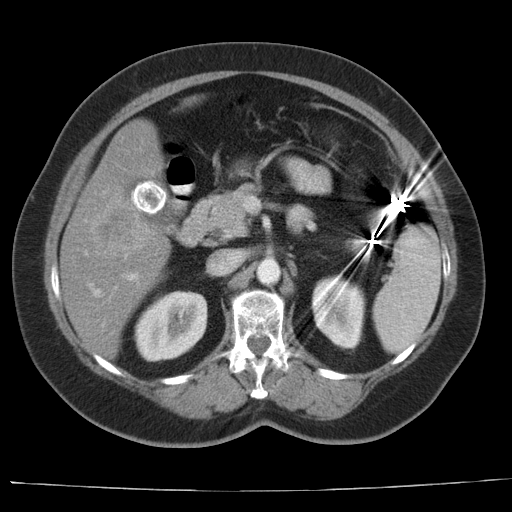
Contrast-enhanced abdominal CT, one axial slice. Slice 15 of 44 in the series (ordered by position). Reconstruction kernel AA-1. 140 kVp. Intravenous contrast given. Soft-tissue window (W 400 / L 40 HU). 5 mm slice thickness. 512 × 512 image matrix, field of view 373 × 373 mm. Female patient. From the clinical record (not read from this slice): diagnosis: colorectal cancer liver metastases, imaged before liver resection; multiple liver metastases: yes; largest metastasis: 1.8 cm; disease in both lobes: no.
Structures marked on this image (expert manual segmentation):
- hepatic veins: box from (x=90, y=286) to (x=100, y=297) px
- liver: (x=60, y=121)–(x=170, y=360)
- planned liver remnant (the part of the liver to remain after resection): (x=103, y=121)–(x=162, y=184)
- portal vein (with intrahepatic branches): (x=127, y=274)–(x=136, y=281)
- liver metastasis: (x=90, y=189)–(x=155, y=251)